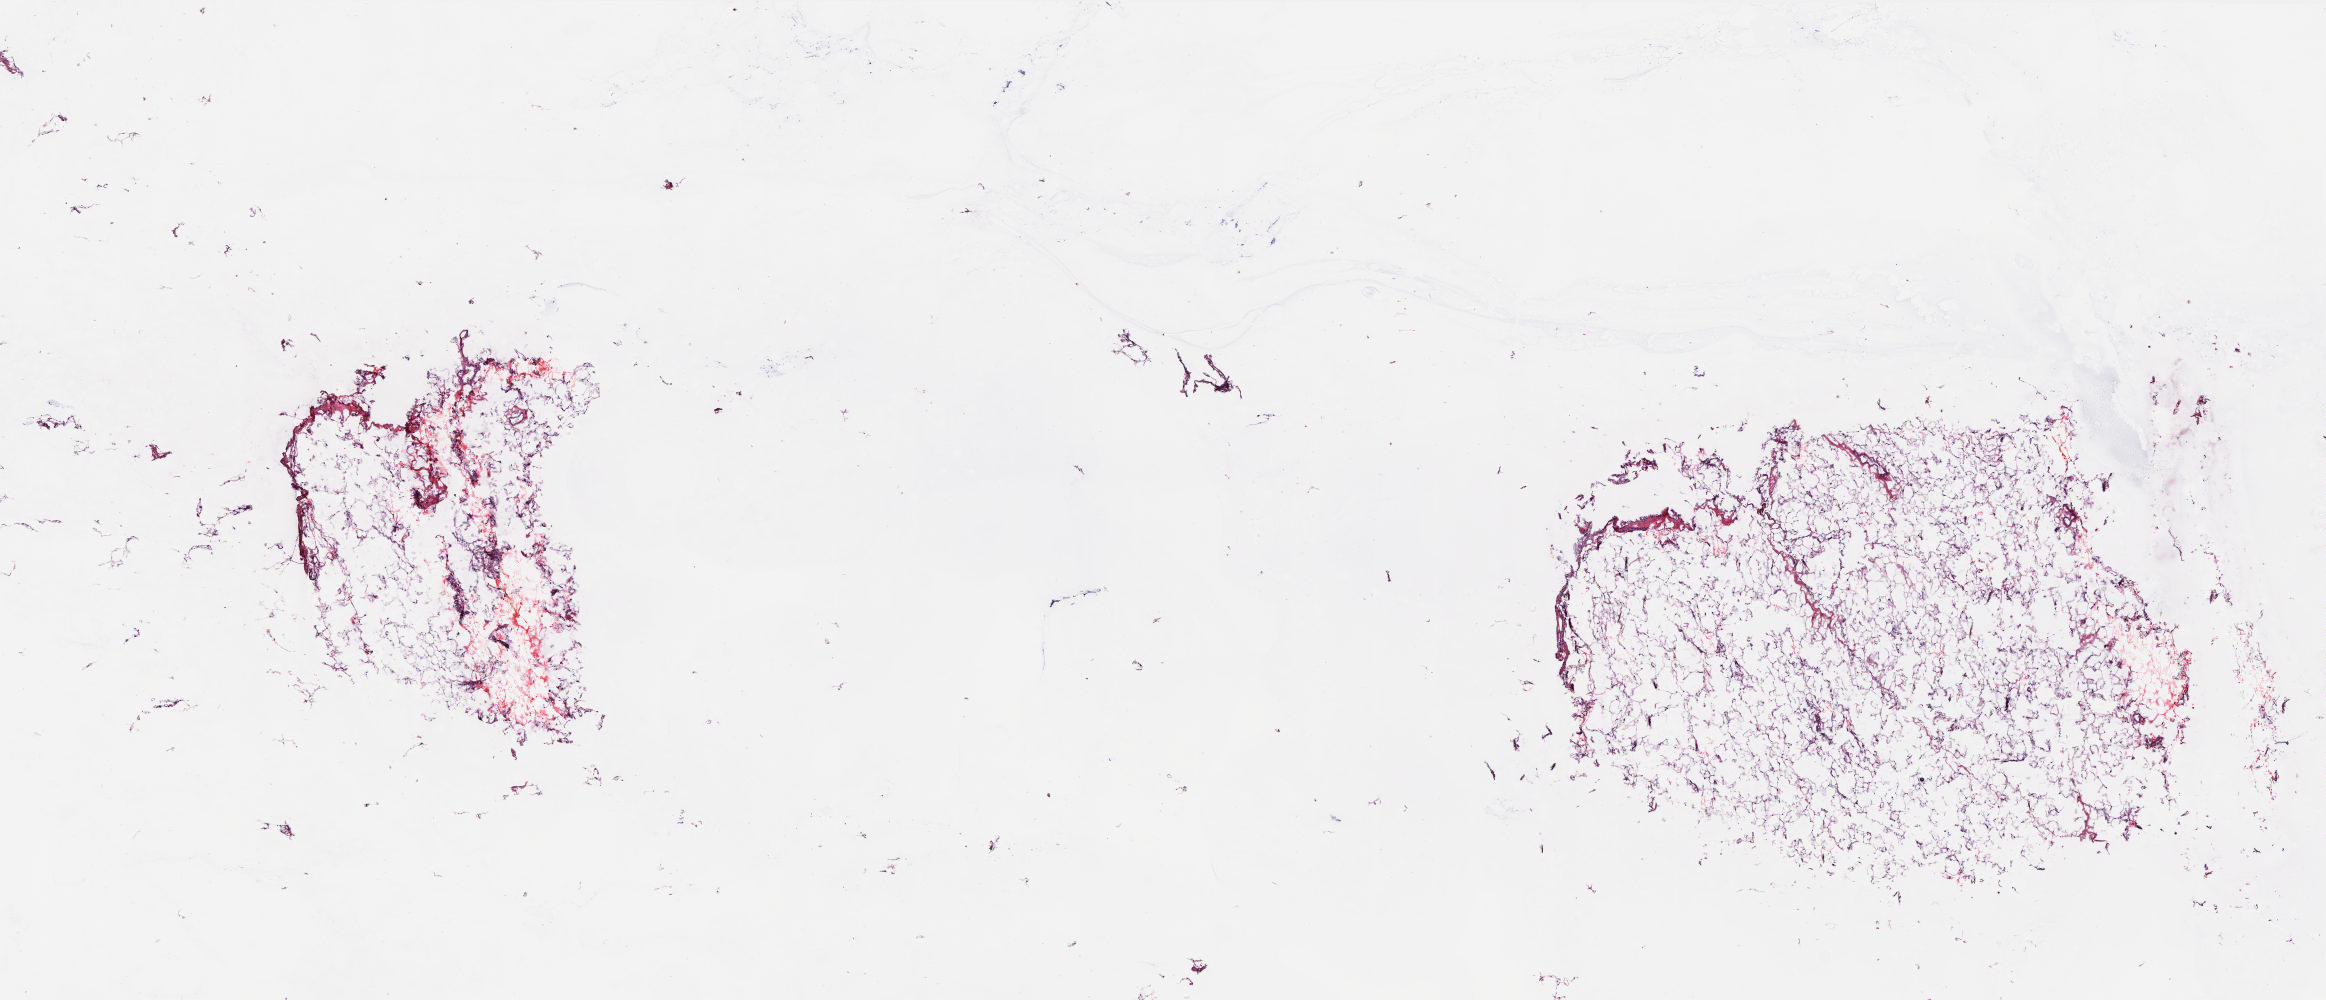
Digitized H&E tissue section (whole slide), a low-resolution overview of the entire scanned area, about 18.8 x 8.1 mm (from a 20x scan); frozen section from the top of the tissue portion; sample: solid tissue normal (non-tumour tissue), connective, subcutaneous and other soft tissues. Male patient; age at initial diagnosis 76 years. Slide review estimates, as recorded: tumour cells 0%, tumour nuclei 0%, normal cells 100%, stromal cells 0%, necrosis 0%. Infiltration values recorded for this section: lymphocyte infiltration 1%, monocyte infiltration 0%, neutrophil infiltration 0%.
This section: solid tissue normal sample (biorepository sample class). Patient diagnosis: Undifferentiated sarcoma (connective, subcutaneous and other soft tissues, NOS).